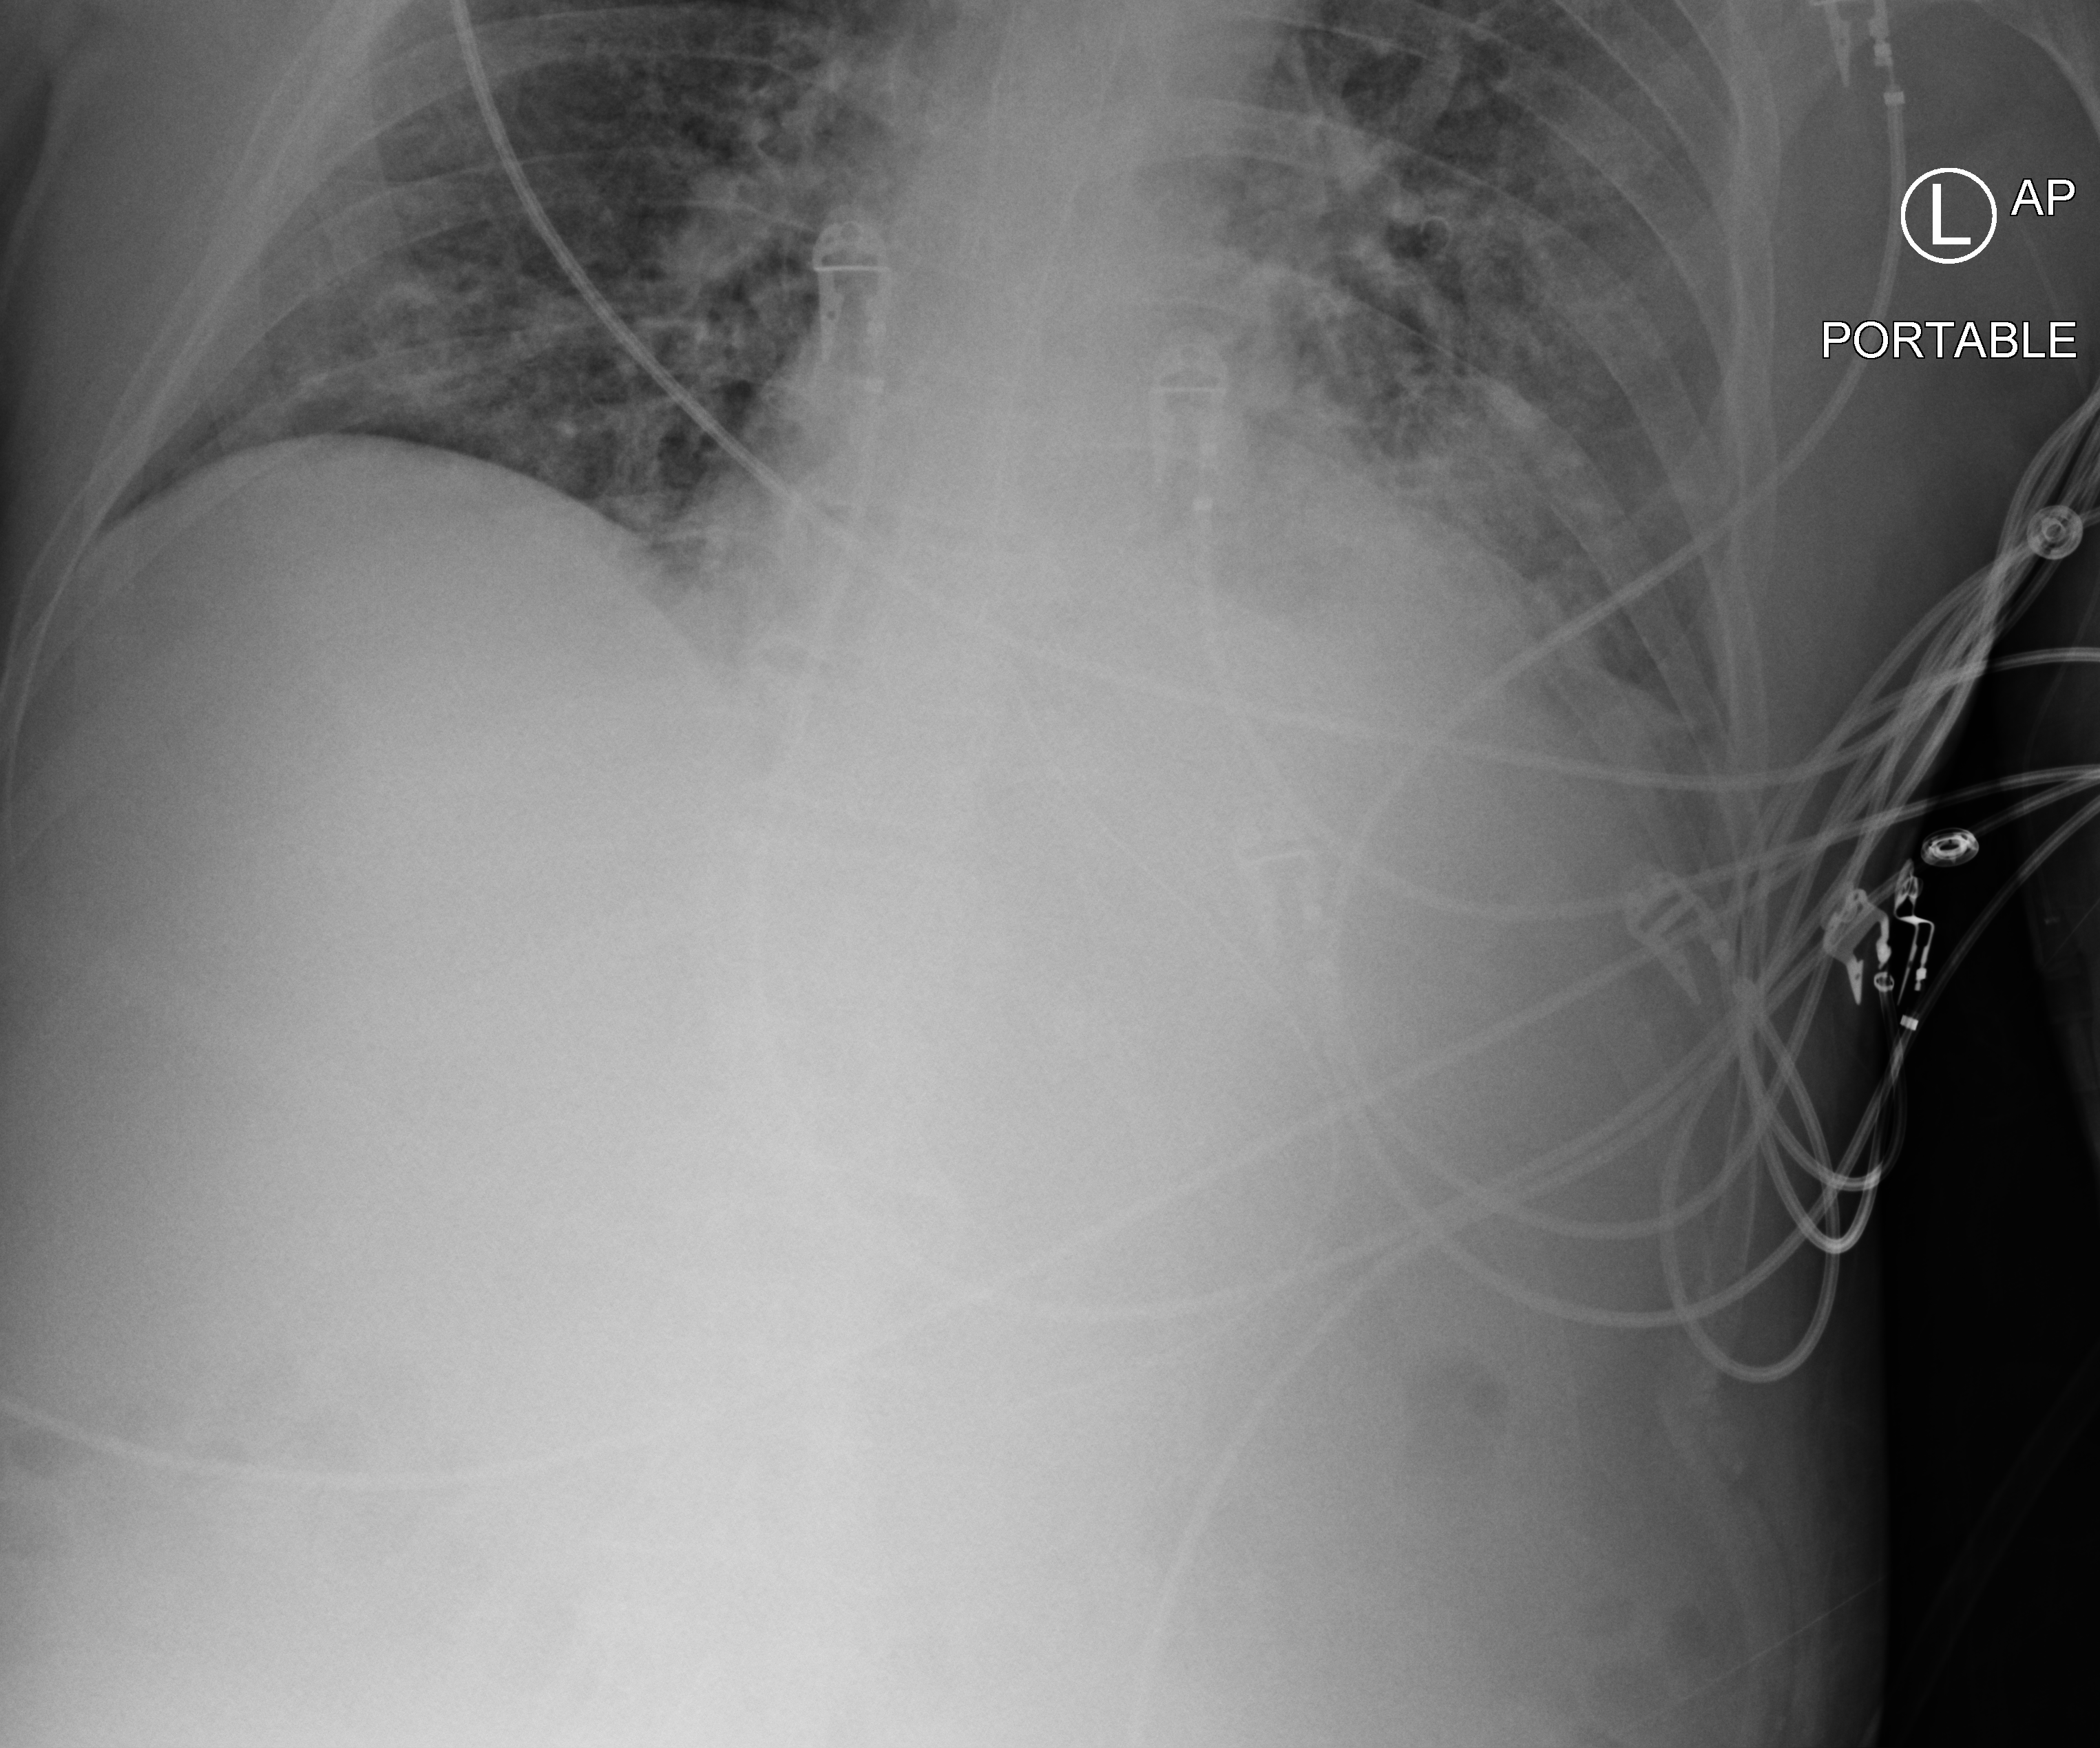
Chest X-ray (portable), anteroposterior (AP) projection. Patient hospitalised with COVID-19; male, aged 18–59 years.
Admission-level facts for this patient (not findings on this image; timing relative to this image not recorded):
- chronic kidney disease (admission record): no
- mechanically ventilated during this hospital stay: yes